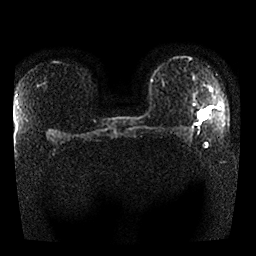
Breast MRI, one axial slice. Position 18 of 25 along the scan axis. Diffusion-weighted series; image 2 of 4 stored at this slice position (different b-values; order by instance number). 1.5 T. 256 × 256 image matrix, field of view 340 × 340 mm. Female patient.
Annotated regions visible in this slice (expert manual segmentation):
- tumour on diffusion-weighted imaging: bounding box (x1, y1, x2, y2) in pixels: (198, 110, 207, 120)